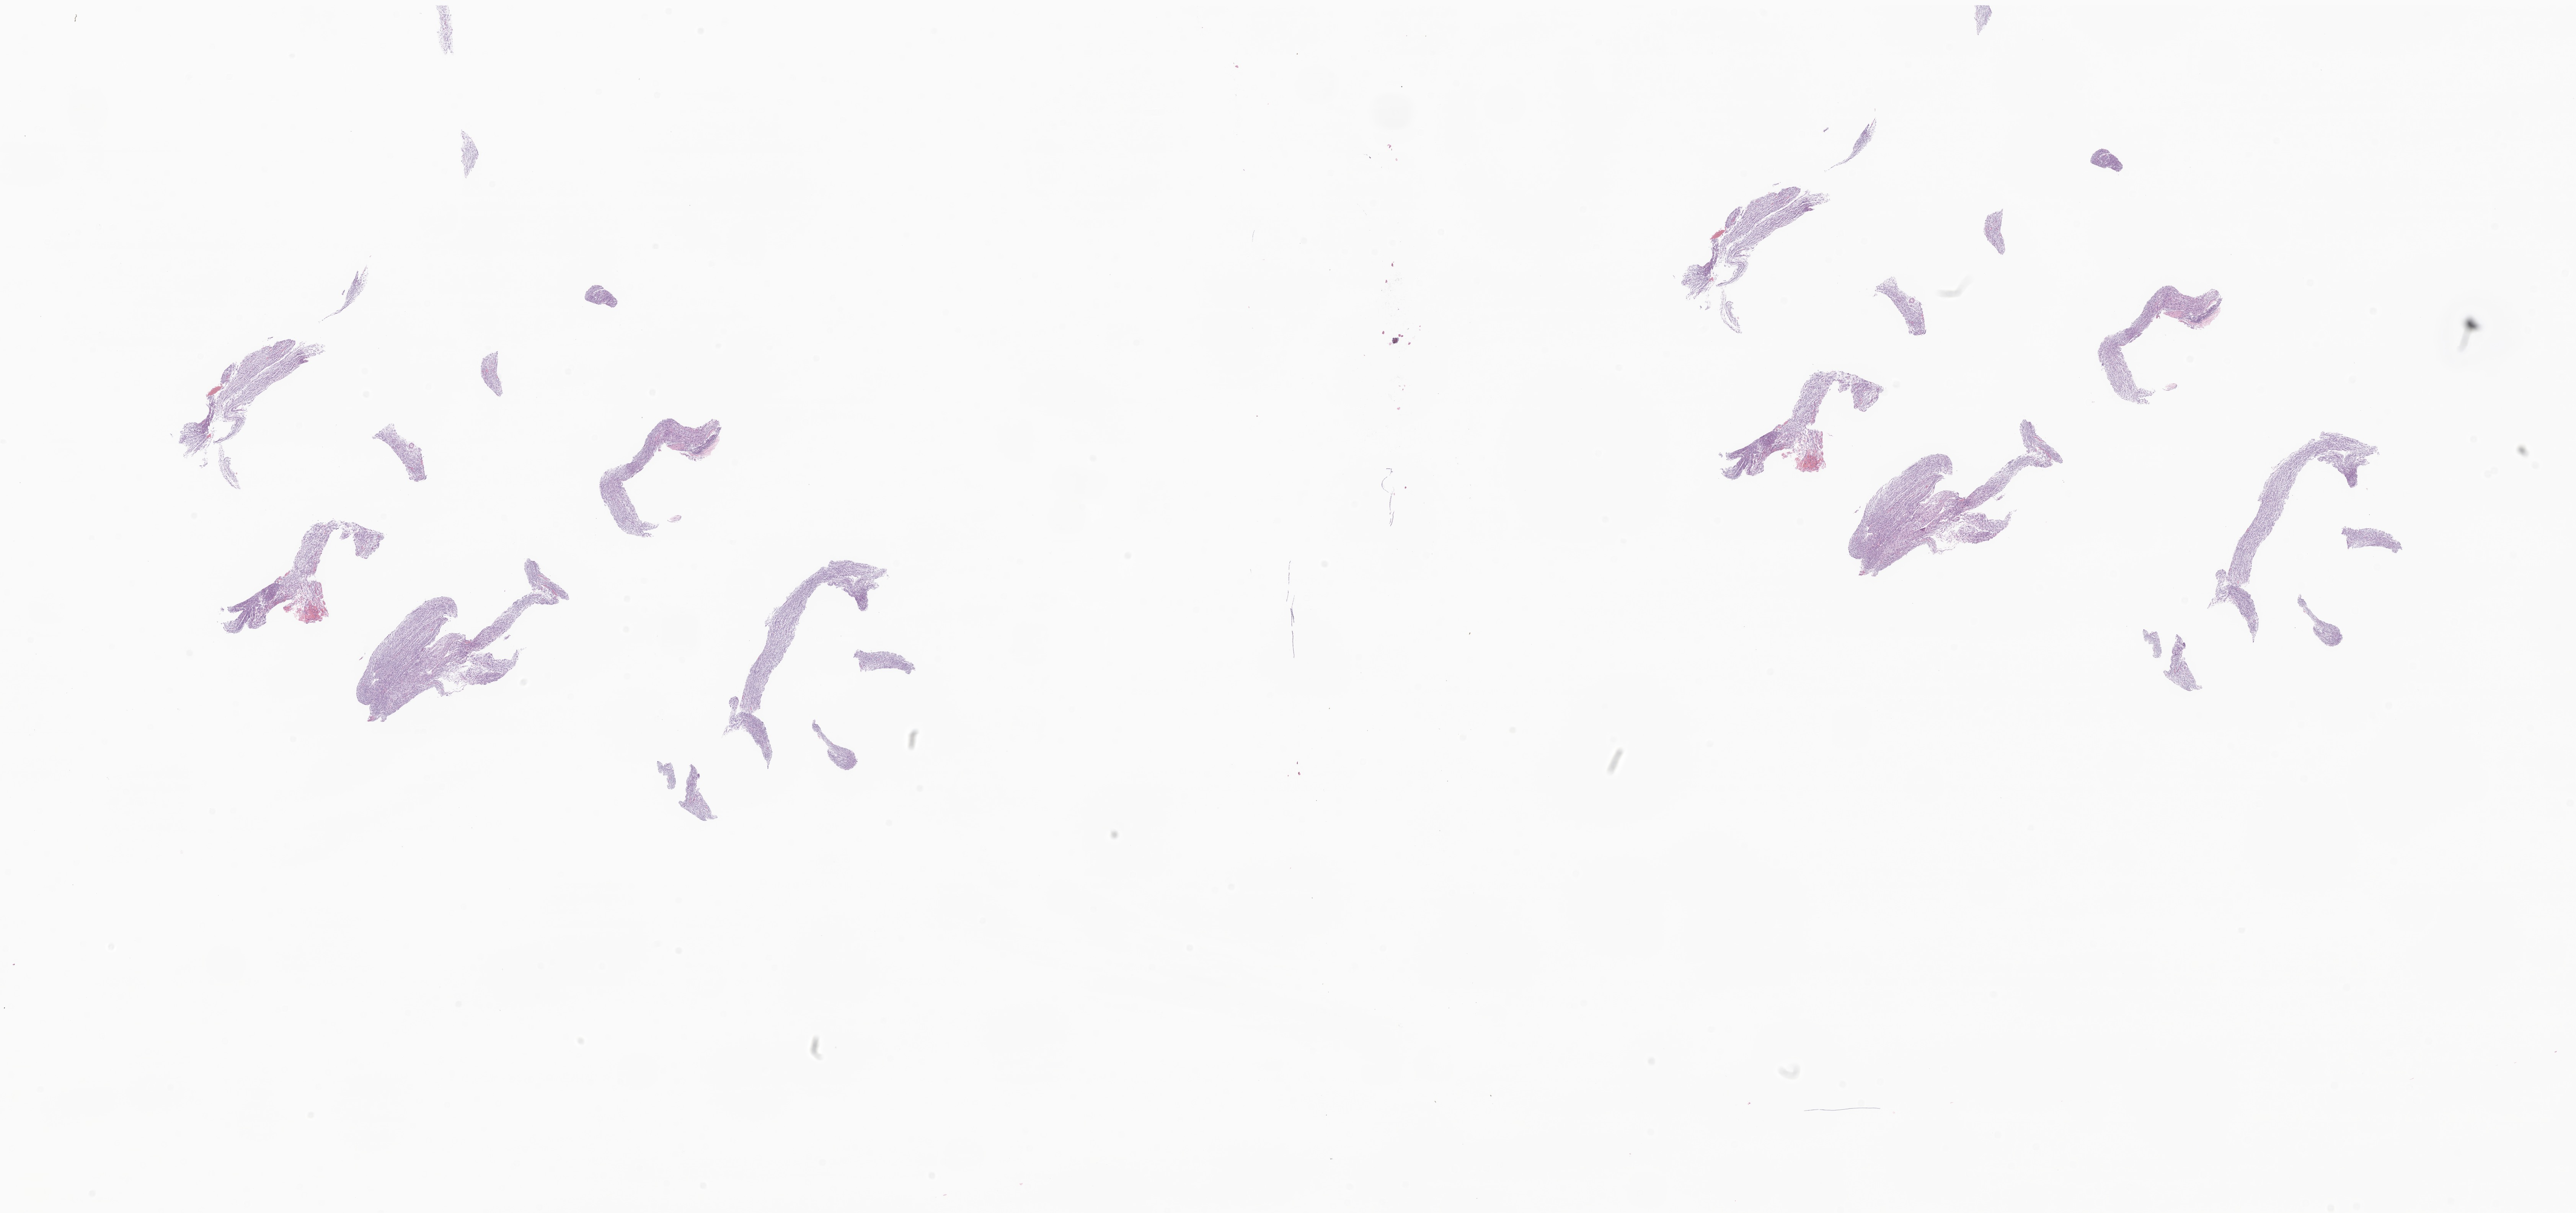
Digitized H&E-stained section of tumor tissue from the soft tissue of upper extremity, whole scanned area (about 28.4 x 13.4 mm) shown as a low-resolution overview; formalin-fixed paraffin-embedded section. Patient: female, age 197 months.
Diagnosis (ICD-O-3 morphology term): Synovial sarcoma, spindle cell.